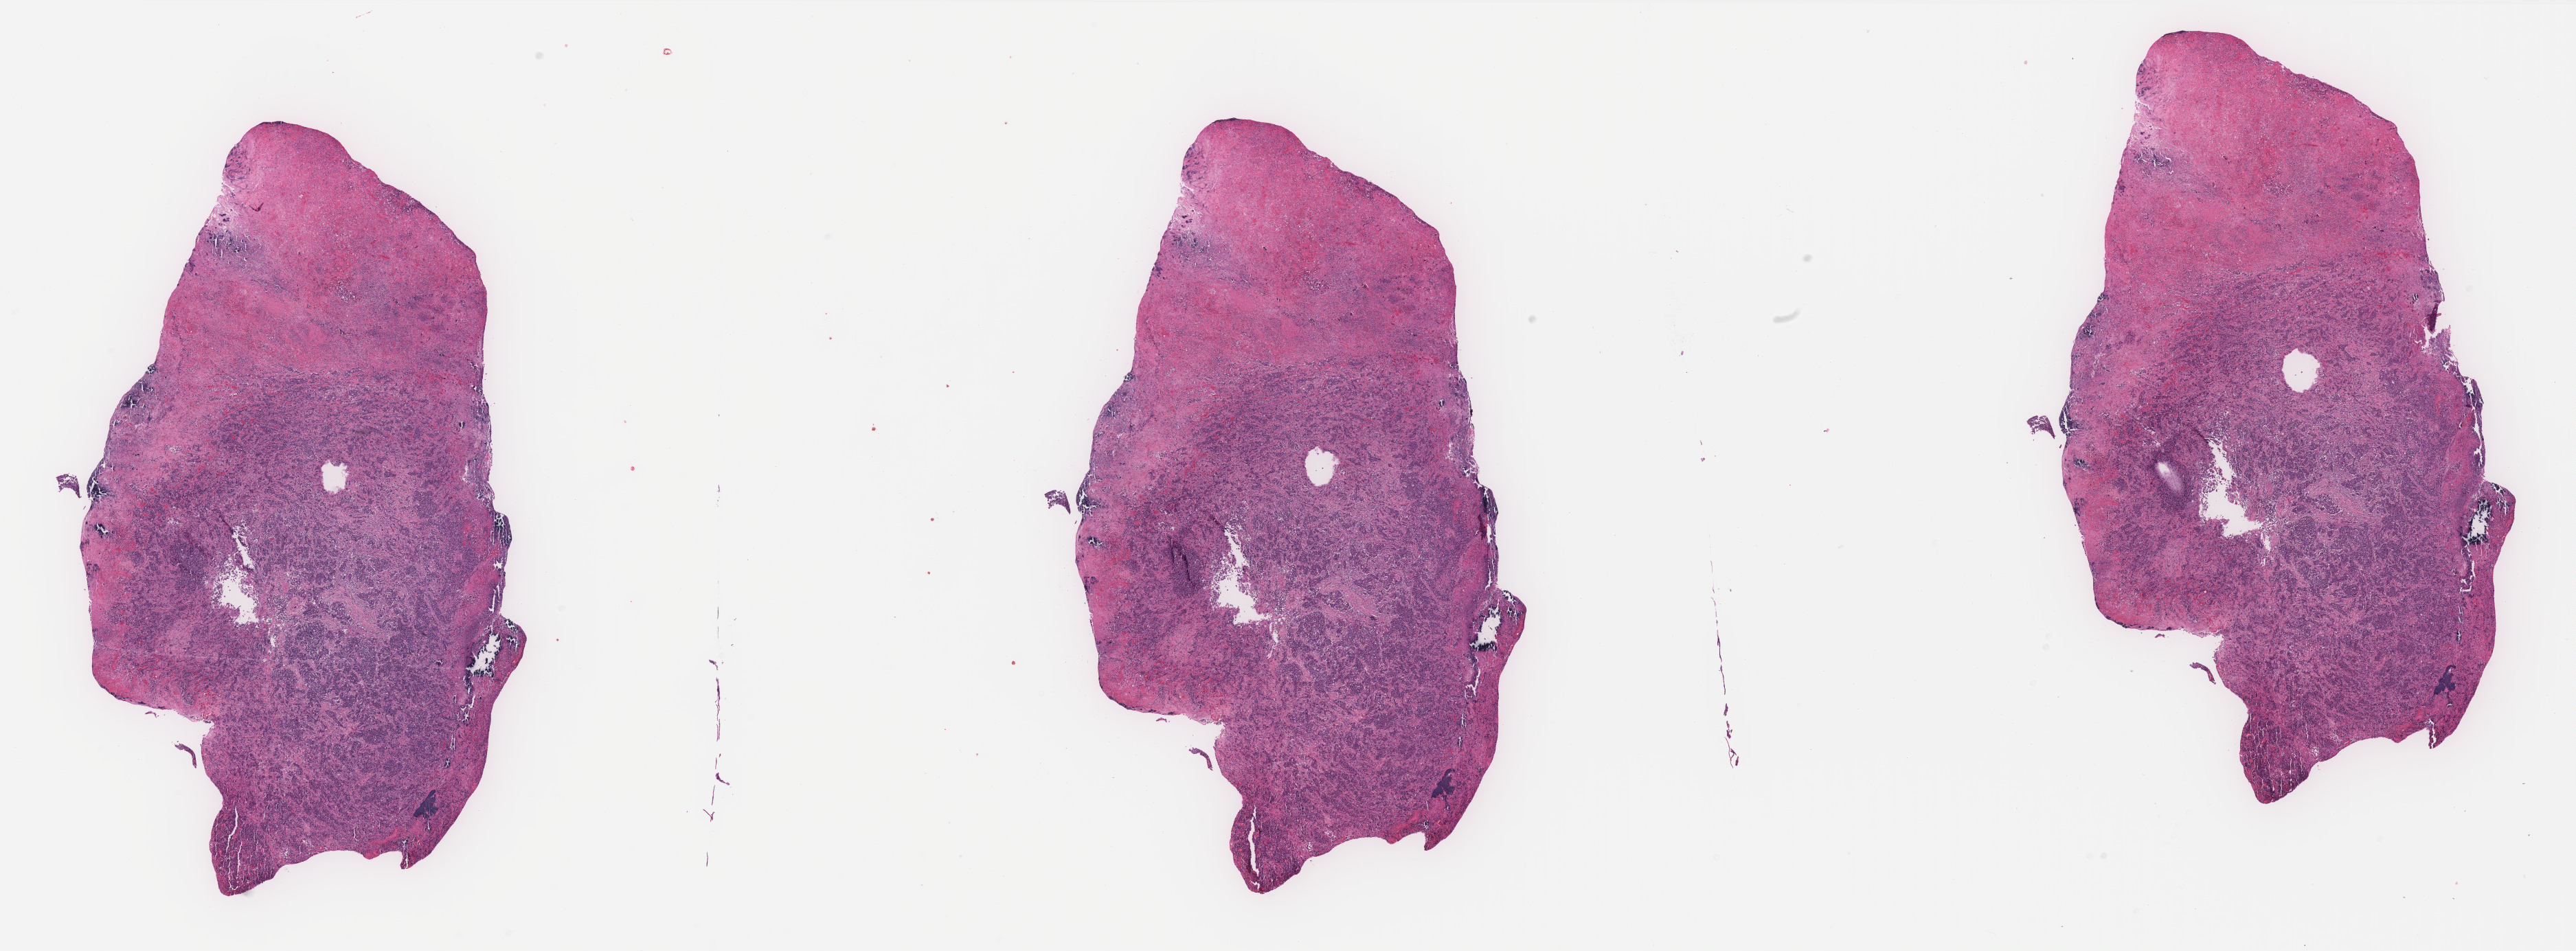
H&E-stained whole-slide image — shown as a low-resolution overview of the whole scanned area (about 30.1 x 11.1 mm, from a 40x scan). Formalin-fixed paraffin-embedded (FFPE) diagnostic section. Bladder, primary tumour sample. Male patient; age at initial diagnosis 83 years. Histologic grade: high grade.
Histologic diagnosis: Transitional cell carcinoma. AJCC pathologic stage: IV.